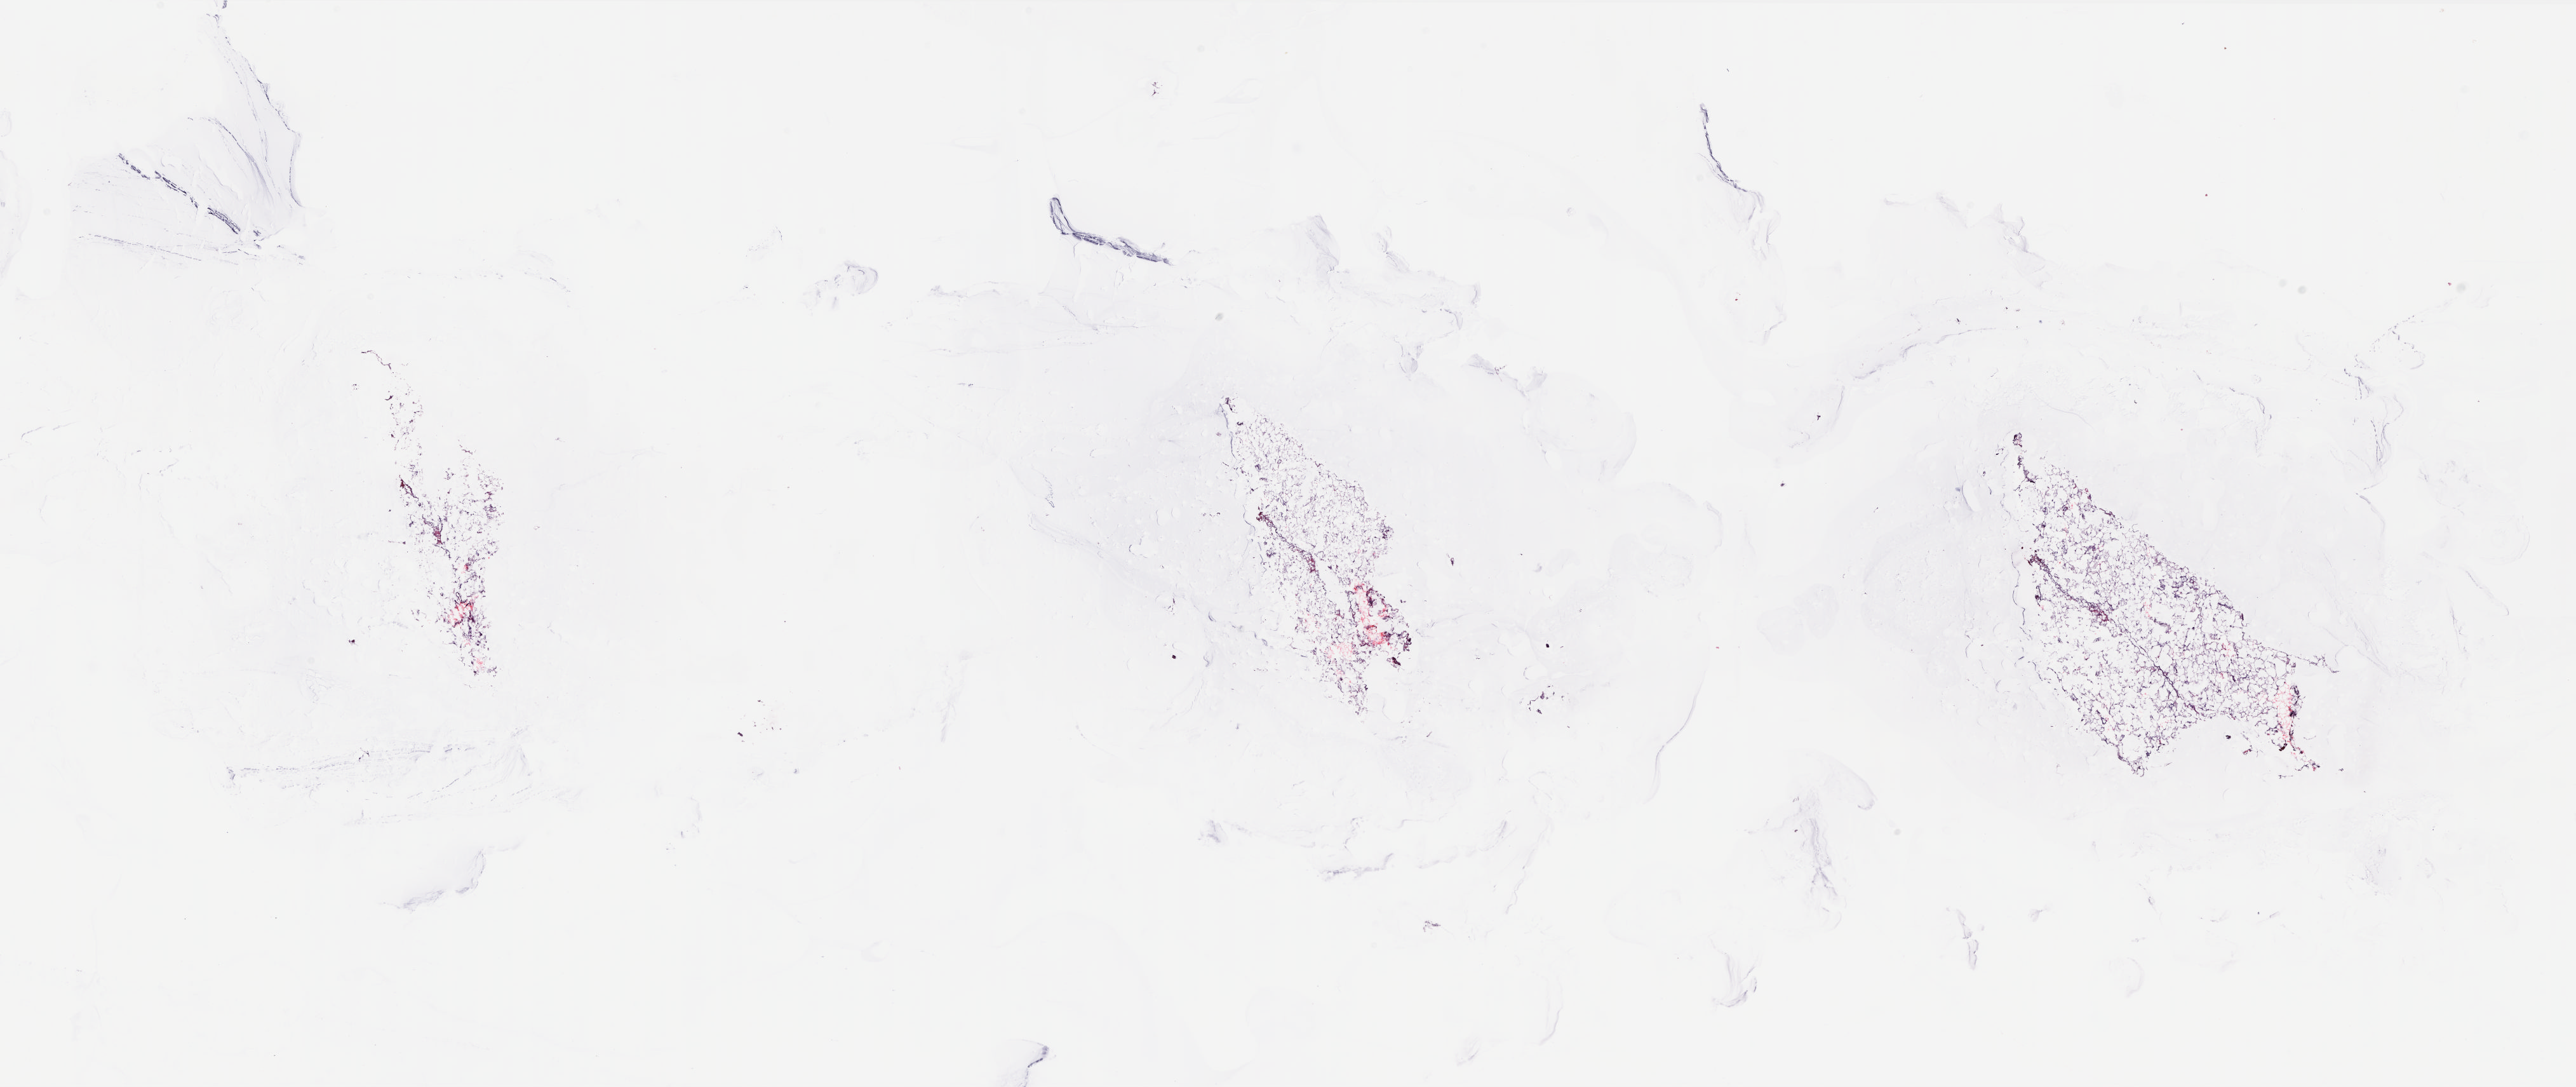
Digitized H&E-stained tissue section (whole slide) — a low-resolution overview of the entire scanned area, about 32.7 x 13.8 mm, frozen section from the top of the tissue portion, sample: solid tissue normal (non-tumour tissue), connective, subcutaneous and other soft tissues. Male, age 76 years at initial diagnosis. Pathologist review of this section (percent, as recorded): tumour cells 0%, tumour nuclei 0%, normal cells 100%, stromal cells 0%, necrosis 0%. Infiltration values recorded for this section: lymphocyte infiltration 1%, monocyte infiltration 0%, neutrophil infiltration 0%.
This section: solid tissue normal sample (biorepository sample class). Patient diagnosis: Undifferentiated sarcoma (connective, subcutaneous and other soft tissues, NOS).